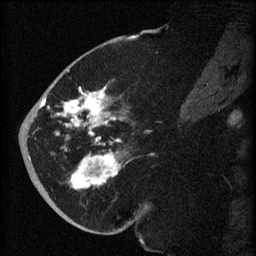
Breast MRI (dynamic contrast-enhanced), one sagittal slice. Slice 29 of 60 in the series (ordered by position). Dynamic contrast-enhanced series, image 2 of 3 at this slice position (ordered by acquisition). 1.5 T. TE 4.2 ms, TR 8.2 ms. 2 mm slice thickness. 256 × 256 image matrix, field of view 180 × 180 mm. Female patient, age 71 years.
Structures marked on this image (semi-automatically segmented with operator editing):
- analysis volume of interest (the breast-tissue region the enhancement analysis was run in; not a lesion): box from (x=40, y=72) to (x=135, y=196) px
- tumour enhancement mask (voxels above the 70 % enhancement threshold inside the analysis volume of interest): (x=40, y=86)–(x=123, y=190)